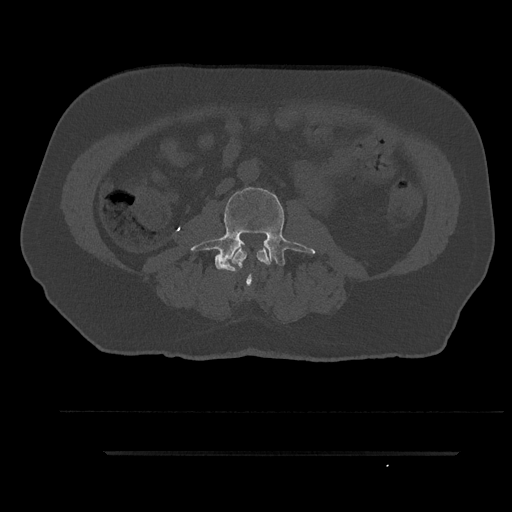
CT including the spine, one axial slice; reconstruction kernel Br40s/3; 120 kVp; bone window (W 1800 / L 400 HU); 512 × 512 image matrix. Patient: male, 63 years. From the clinical record (not read from this slice): primary cancer: renal.
Annotated regions visible in this slice (semi-automatic segmentation, software-assisted and operator-edited):
- L2 vertebra: box from (x=232, y=248) to (x=270, y=272) px
- L3 vertebra: (x=190, y=185)–(x=315, y=285)